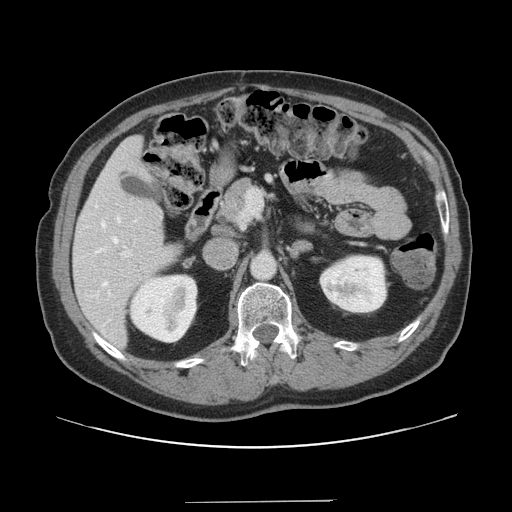
Contrast-enhanced abdominal CT, one axial slice; slice 76 of 151 in the series (ordered by position); intravenous contrast given; soft-tissue window (W 400 / L 40 HU); 2.5 mm slice thickness; 512 × 512 image matrix, field of view 399 × 399 mm. Male patient, age 63 years. Case-level facts recorded for this patient, not image findings: diagnosis: colorectal cancer liver metastases, imaged before liver resection; multiple liver metastases: no; largest metastasis: 2.1 cm; disease in both lobes: no.
Structures marked on this image (outlined manually by an expert reader):
- hepatic veins: bounding box [x1, y1, x2, y2] px = [101, 216, 120, 286]
- liver: [74, 137, 181, 348]
- planned liver remnant (the part of the liver to remain after resection): [74, 137, 181, 348]
- portal vein (with intrahepatic branches): [121, 191, 261, 258]